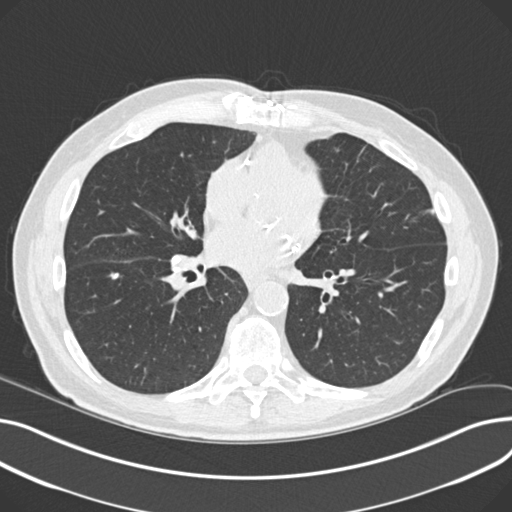
Low-dose screening chest CT, one axial slice; slice 99 of 230 in the series (ordered by position); reconstruction kernel B30f; 120 kVp; lung window (W 1500 / L -600 HU); 512 × 512 image matrix.
Annotated regions visible in this slice (expert manual segmentation):
- lesion 2 (tumor, lower lobe of right lung): box from (x=110, y=273) to (x=121, y=280) px